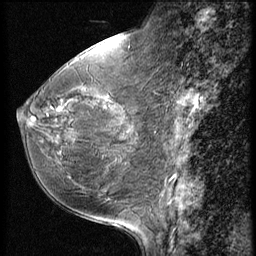
Breast MRI (dynamic contrast-enhanced), one sagittal slice; slice 22 of 56 in the series (ordered by position); 3 images stored at this slice position (order not interpretable as contrast timing); 1.5 T; TE 4.2 ms, TR 9 ms; 2.5 mm slice thickness; 256 × 256 image matrix. Patient: female, 49 years. From the clinical record (not read from this slice): setting: breast cancer imaged before/during neoadjuvant chemotherapy; receptor status: HER2-positive.
Structures marked on this image (semi-automatic segmentation, software-assisted and operator-edited):
- analysis volume of interest (the breast-tissue region the enhancement analysis was run in; not a lesion): bounding box [x1, y1, x2, y2] px = [18, 74, 148, 198]
- tumour enhancement mask (voxels above the 140 % enhancement threshold inside the analysis volume of interest): [32, 108, 63, 122]